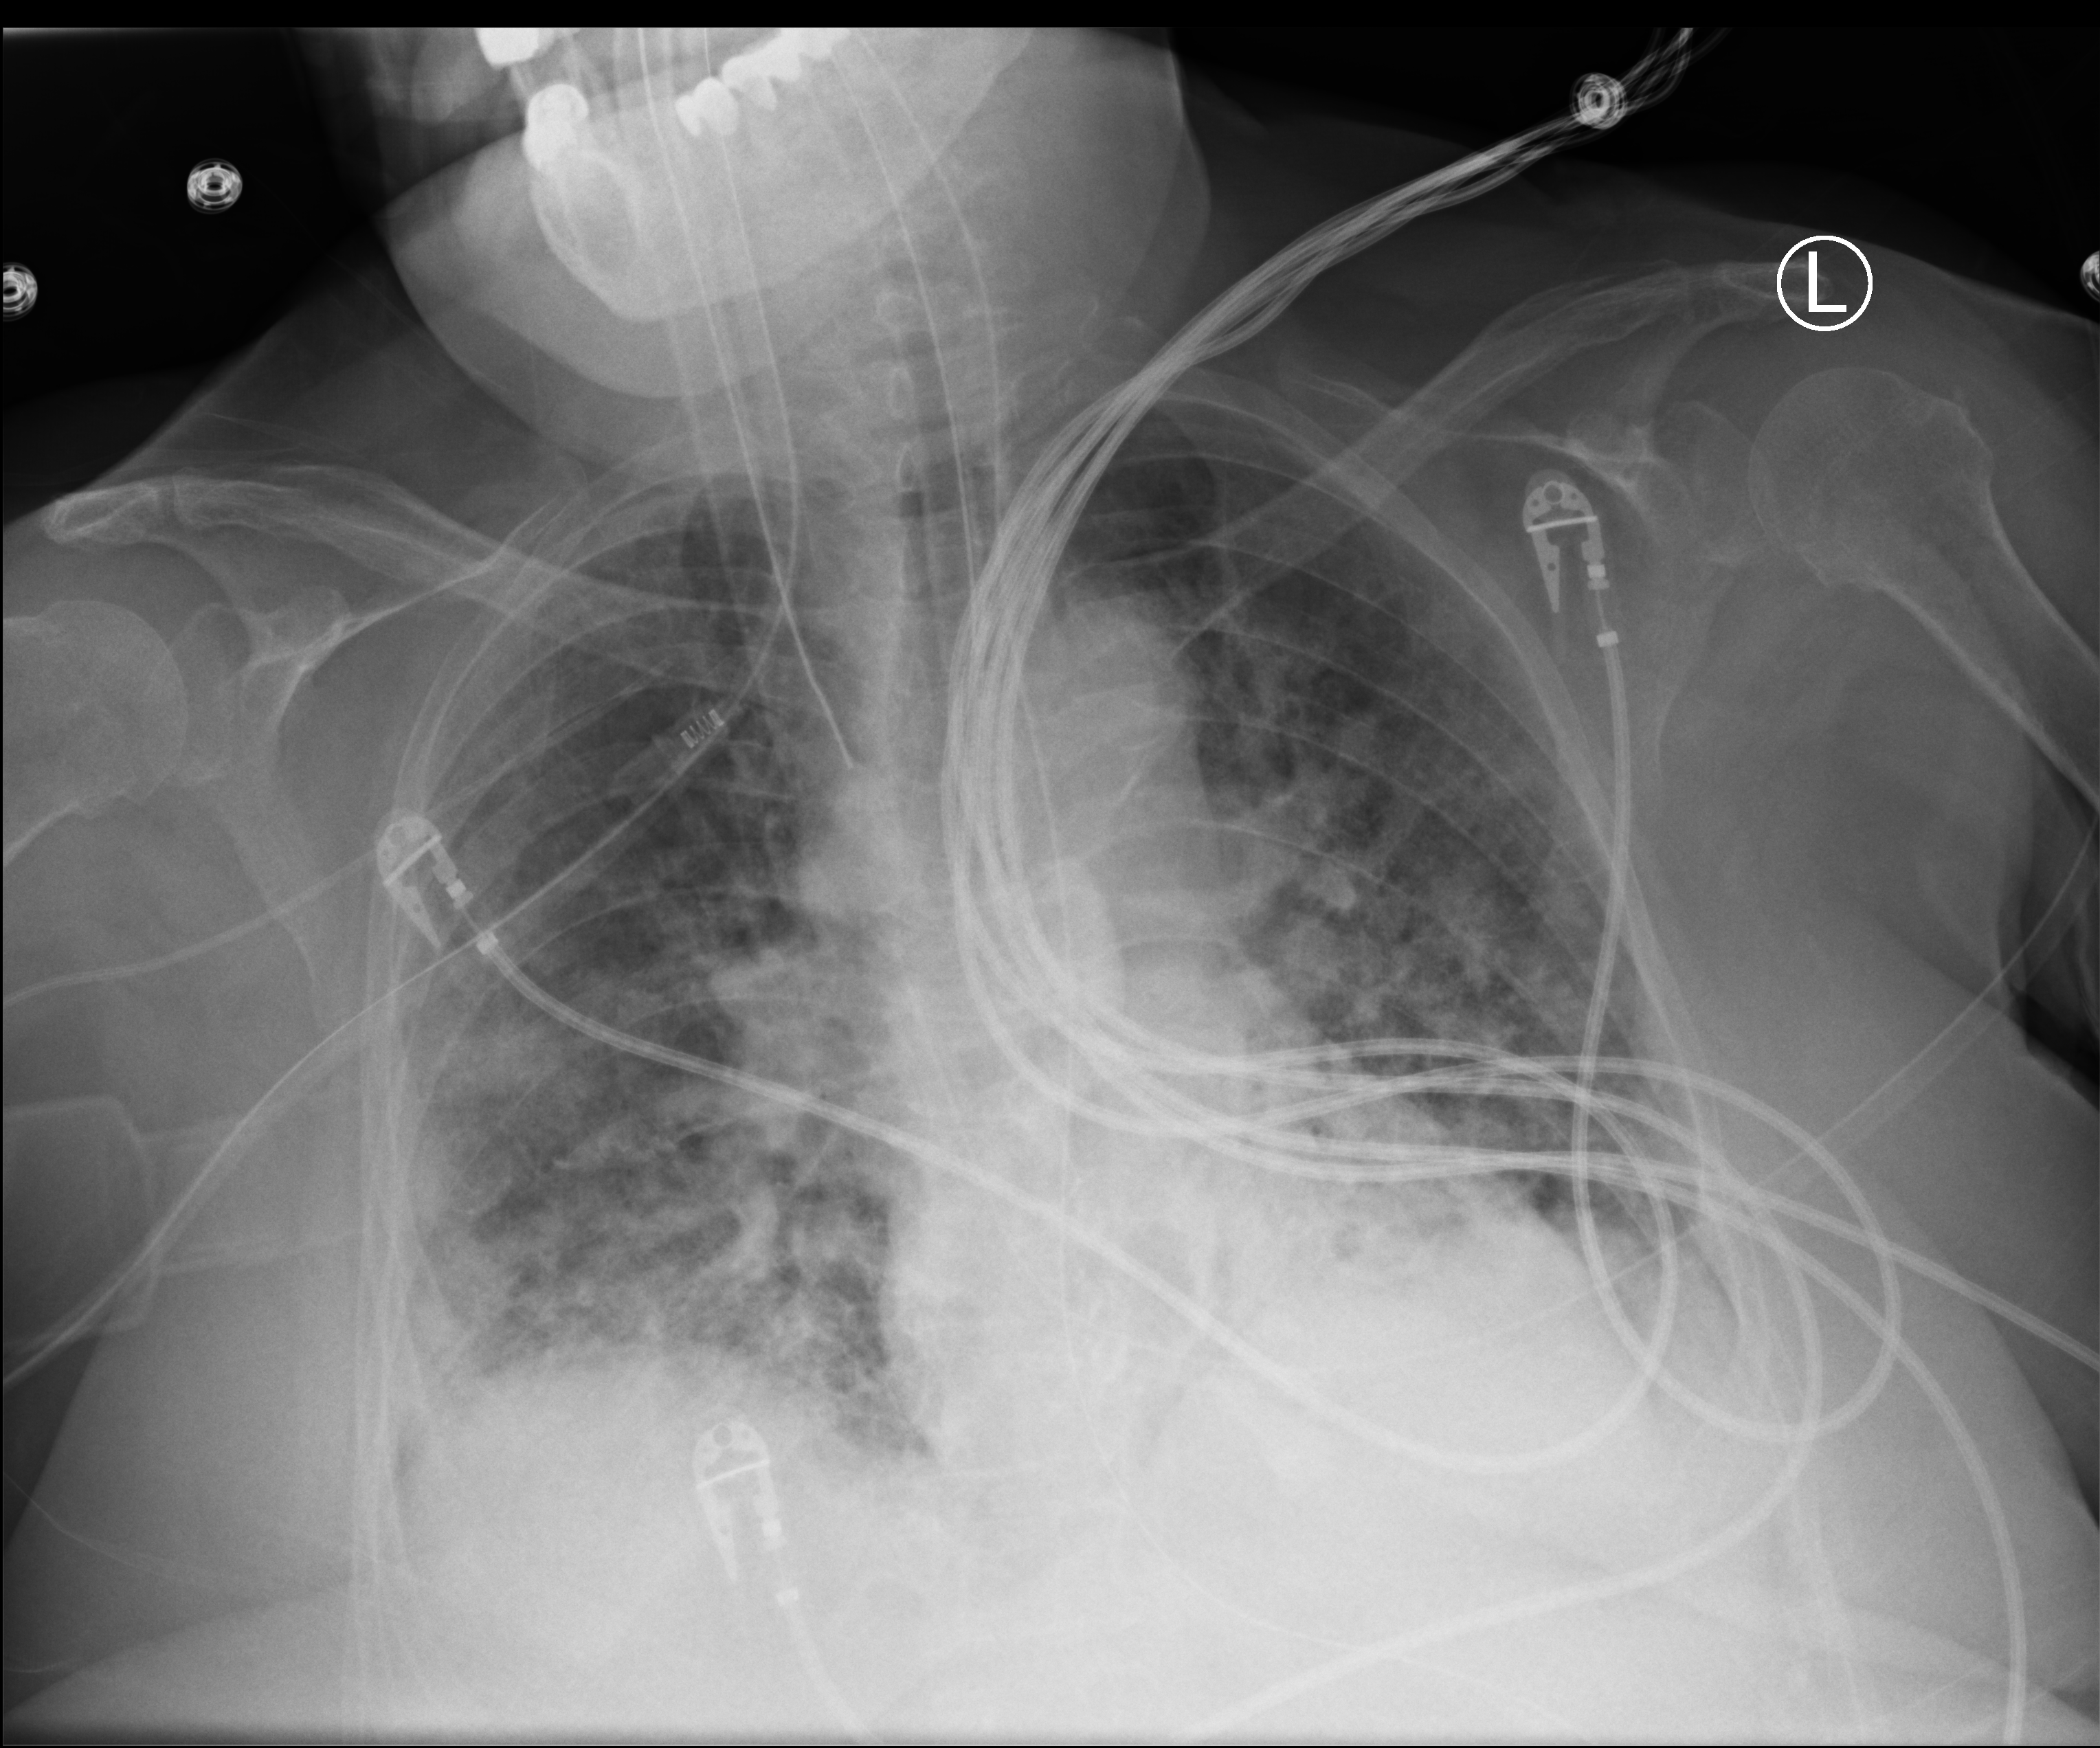
Portable chest radiograph. Female patient hospitalised with COVID-19, age 60–74 years.
From the hospital-stay record, not from the radiograph (when in the stay this image was taken is not recorded): diabetes (admission record): yes; admitted to intensive care during this hospital stay: yes; smoking status (admission record): never.